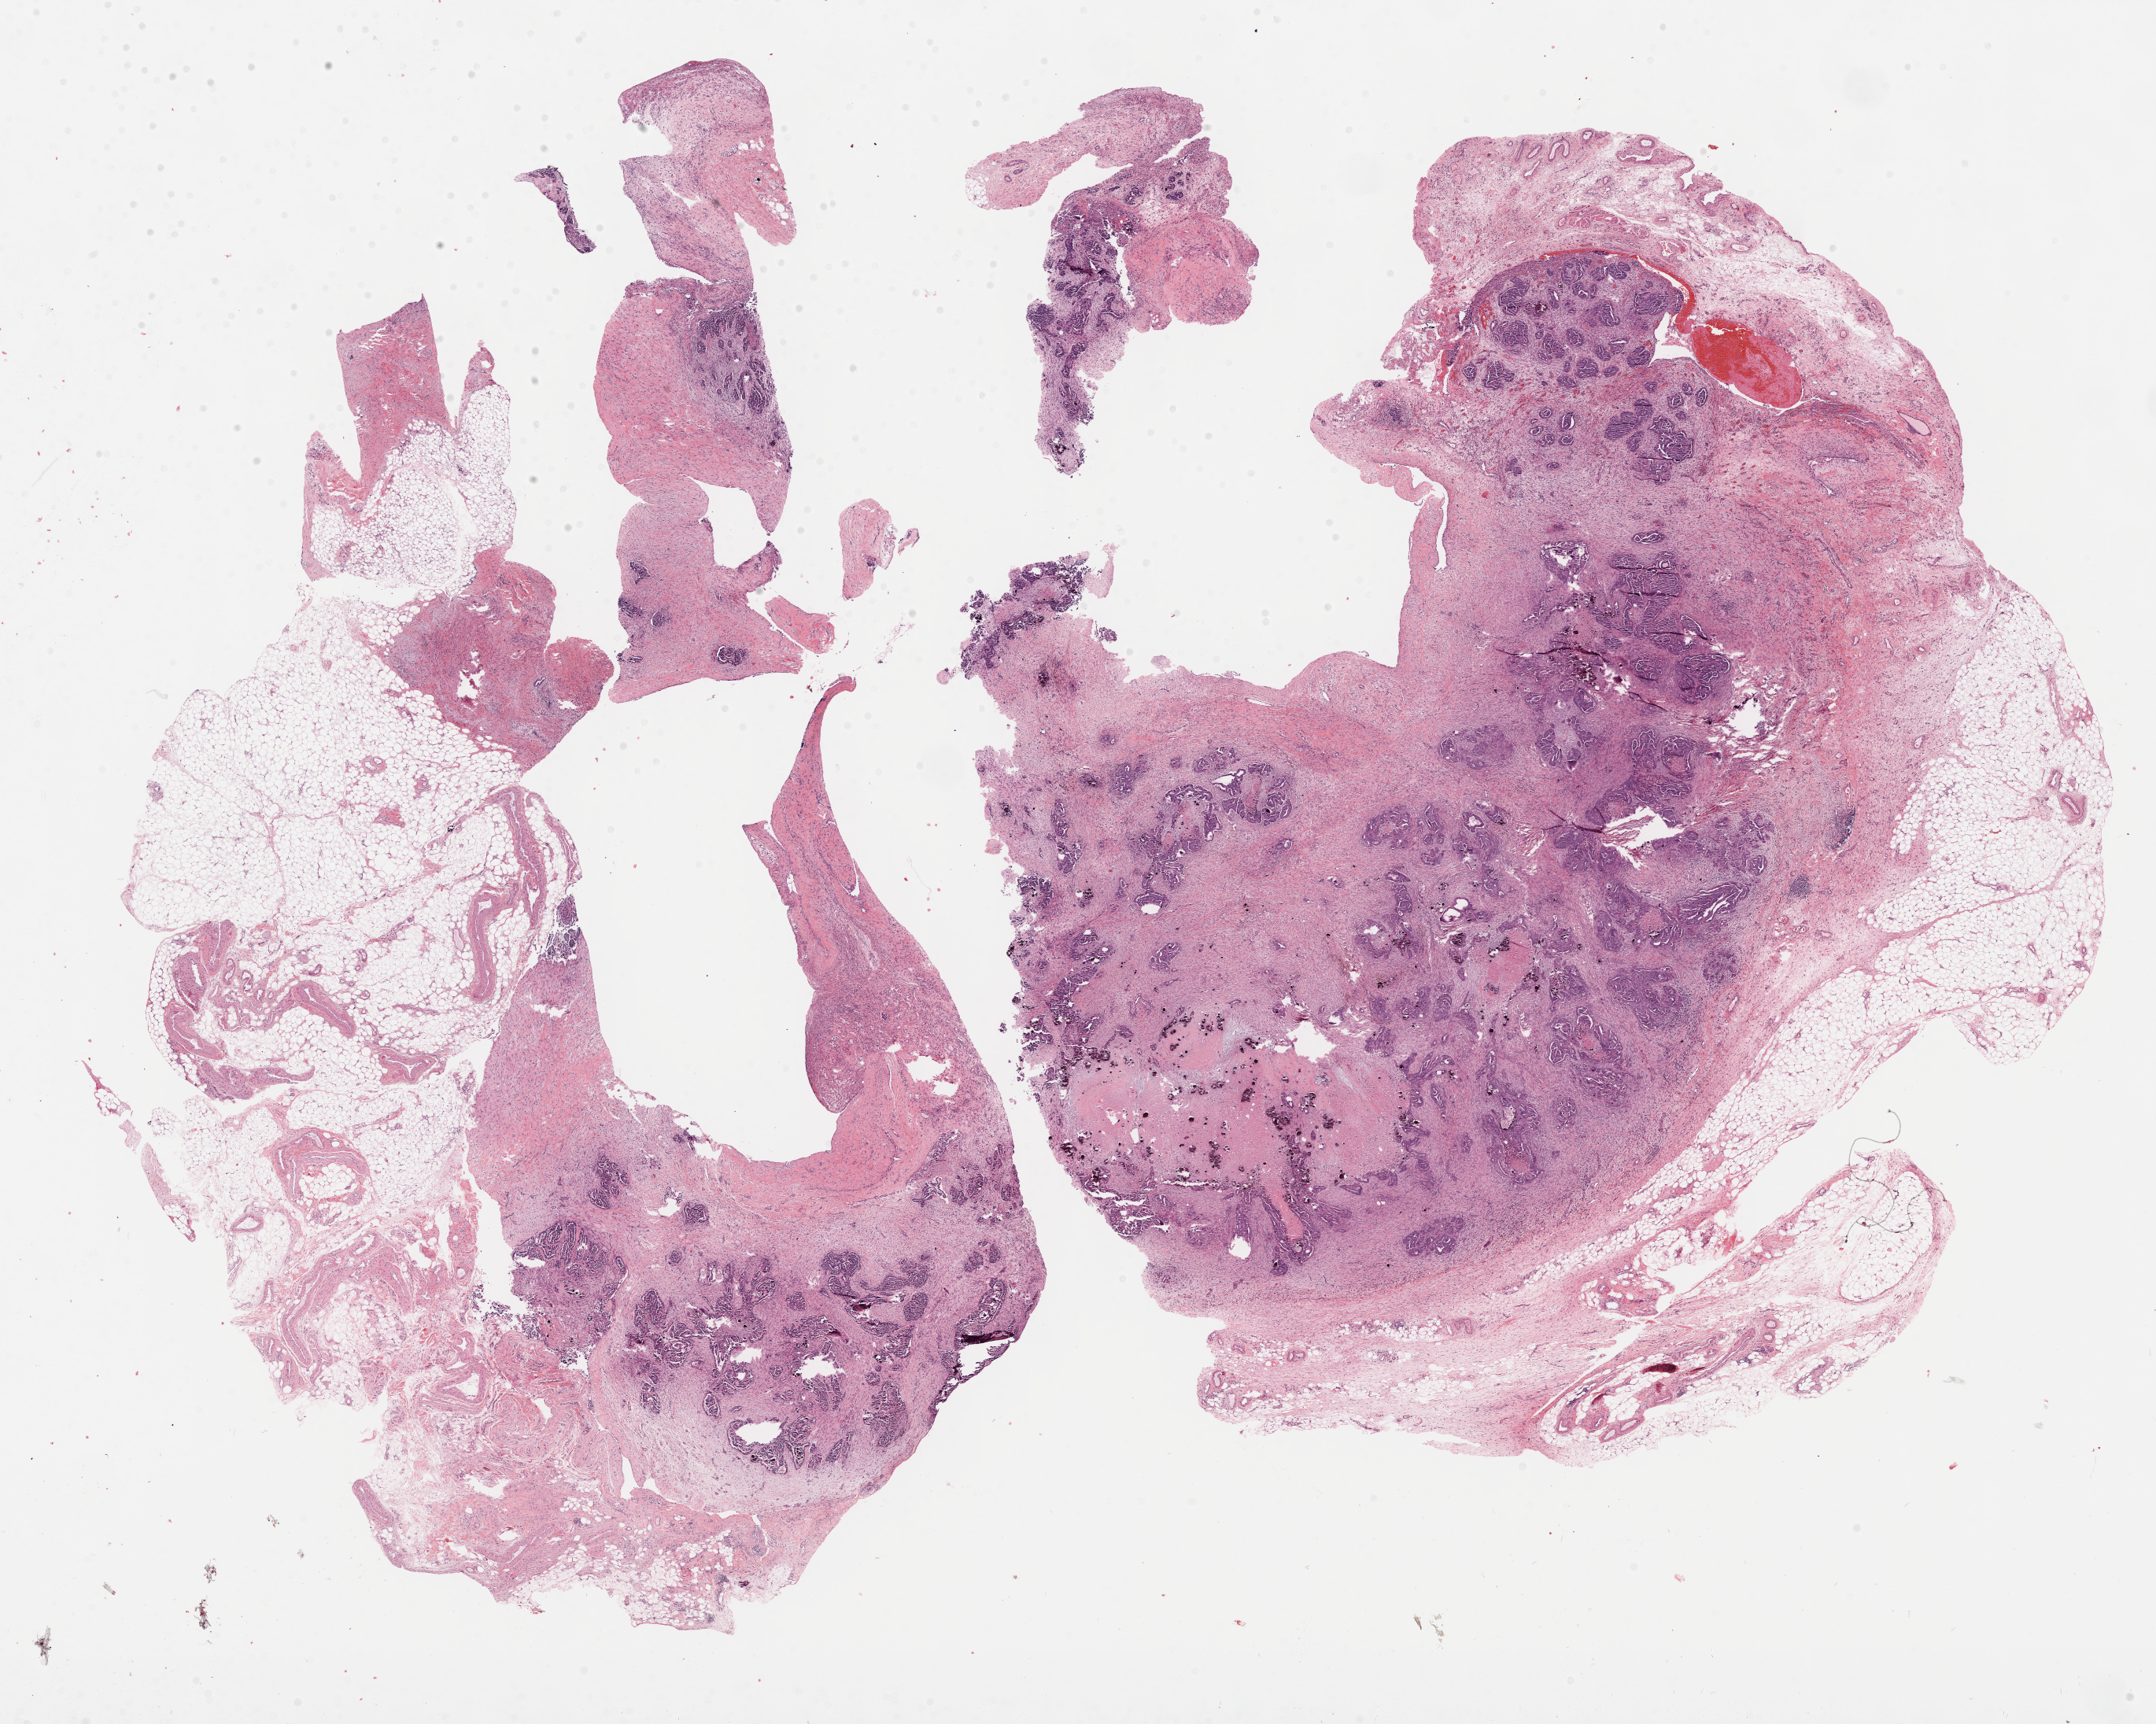
Digitized H&E-stained tissue section (whole slide) — low-resolution overview of the scanned area, about 22.1 x 17.7 mm (from a 40x scan). Formalin-fixed paraffin-embedded (FFPE) diagnostic section. Sample: primary tumour, ovary. Patient: female, age at initial diagnosis 71 years. Histologic grade: G3 (poorly differentiated).
• FIGO stage: IIIC
• histologic diagnosis: Serous cystadenocarcinoma, NOS